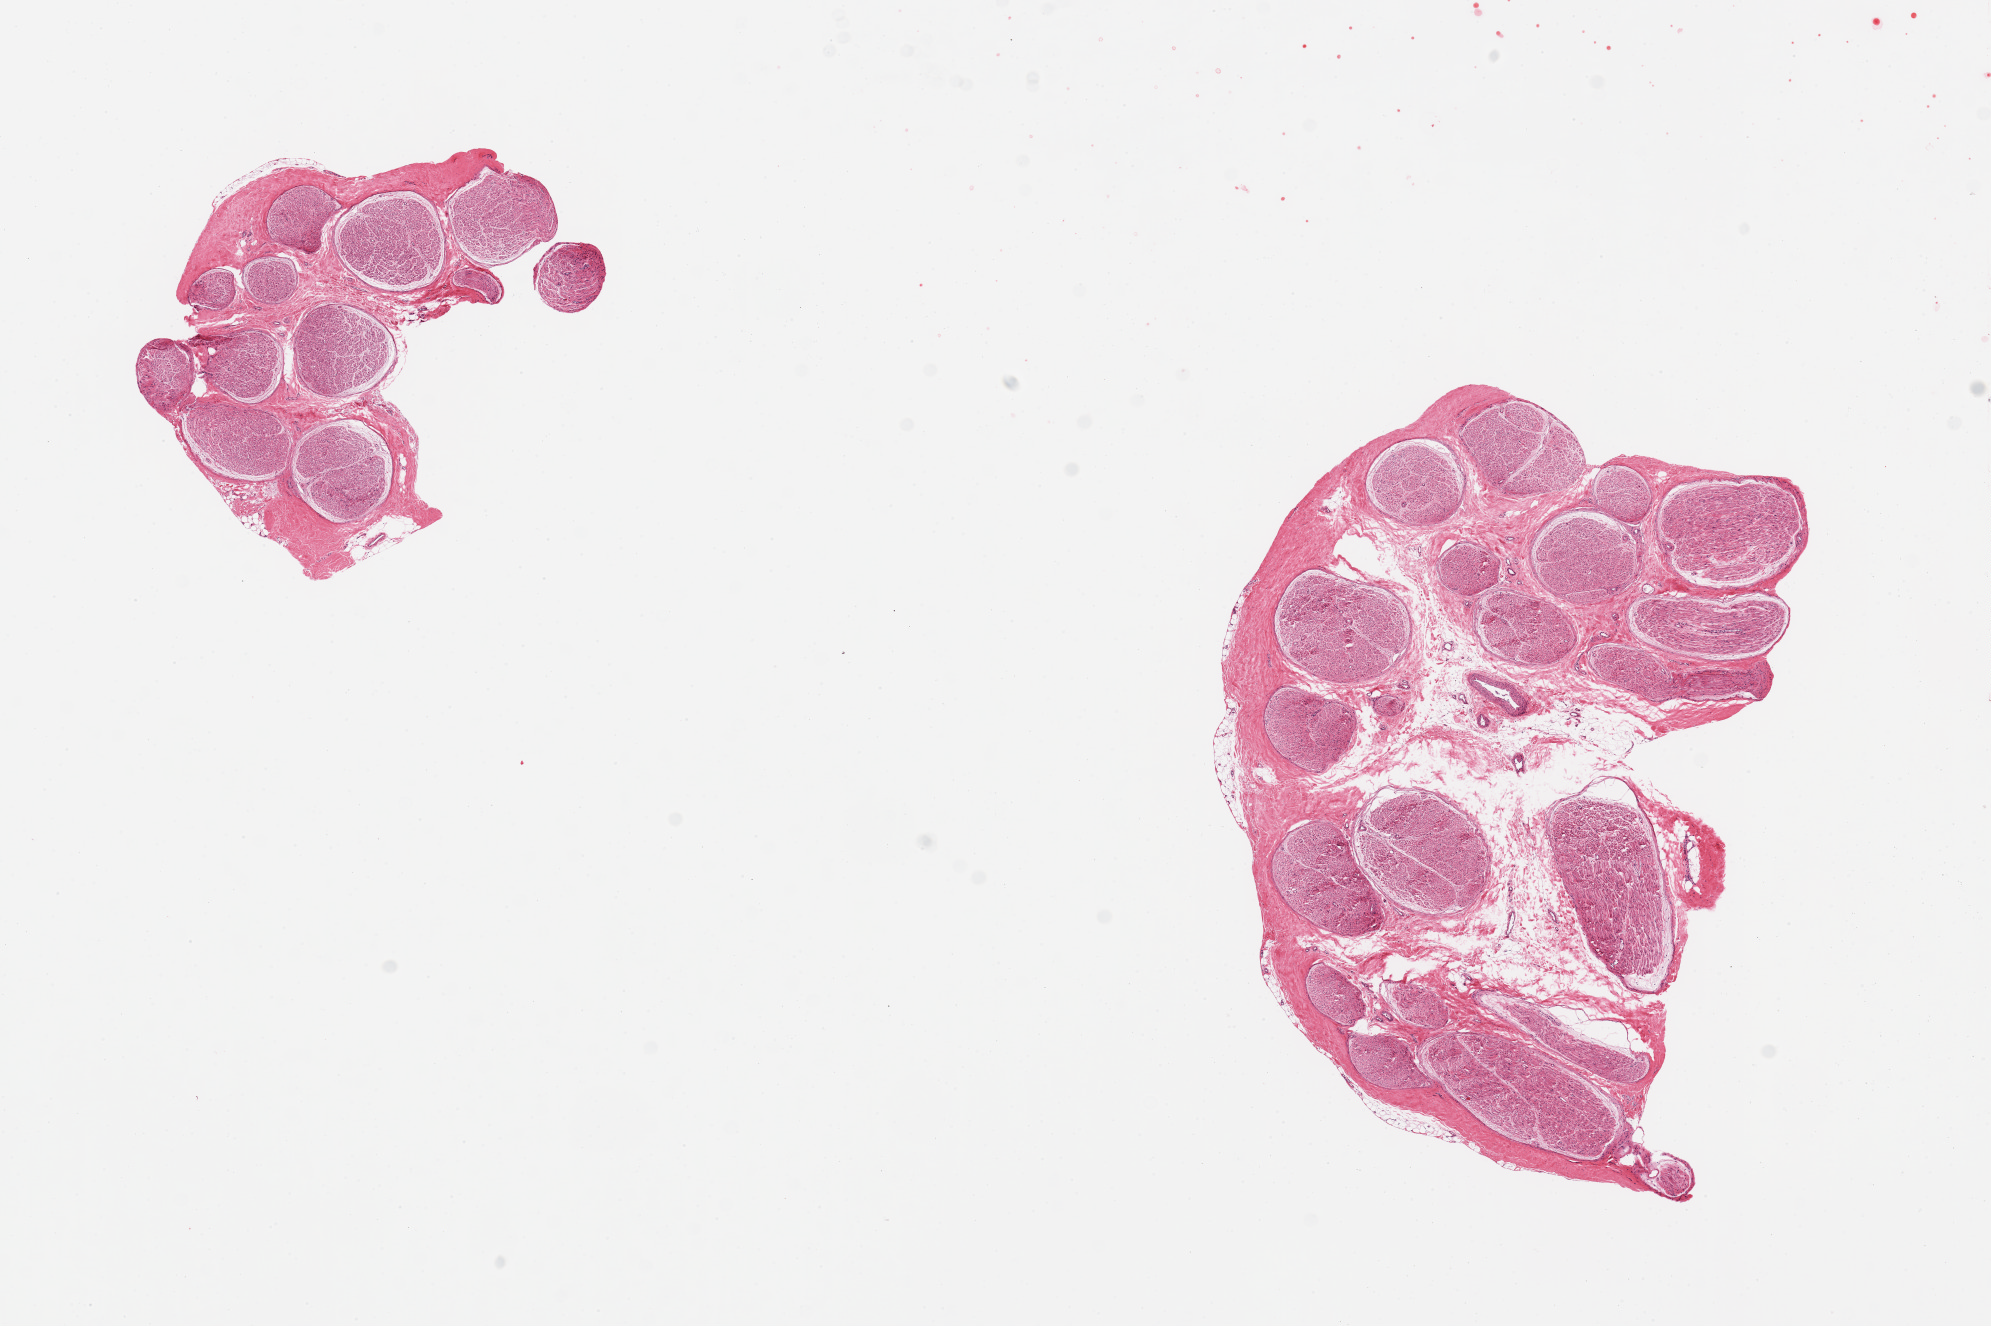
Haematoxylin and eosin whole-slide image — shown as a low-resolution overview of the whole scanned area (about 15.8 x 10.5 mm, from a 20x scan); PAXgene-fixed, paraffin-embedded tissue; section of tibial nerve (target tissue); donor tissue sample. Donor: male.
- review note (as recorded): 2 pieces